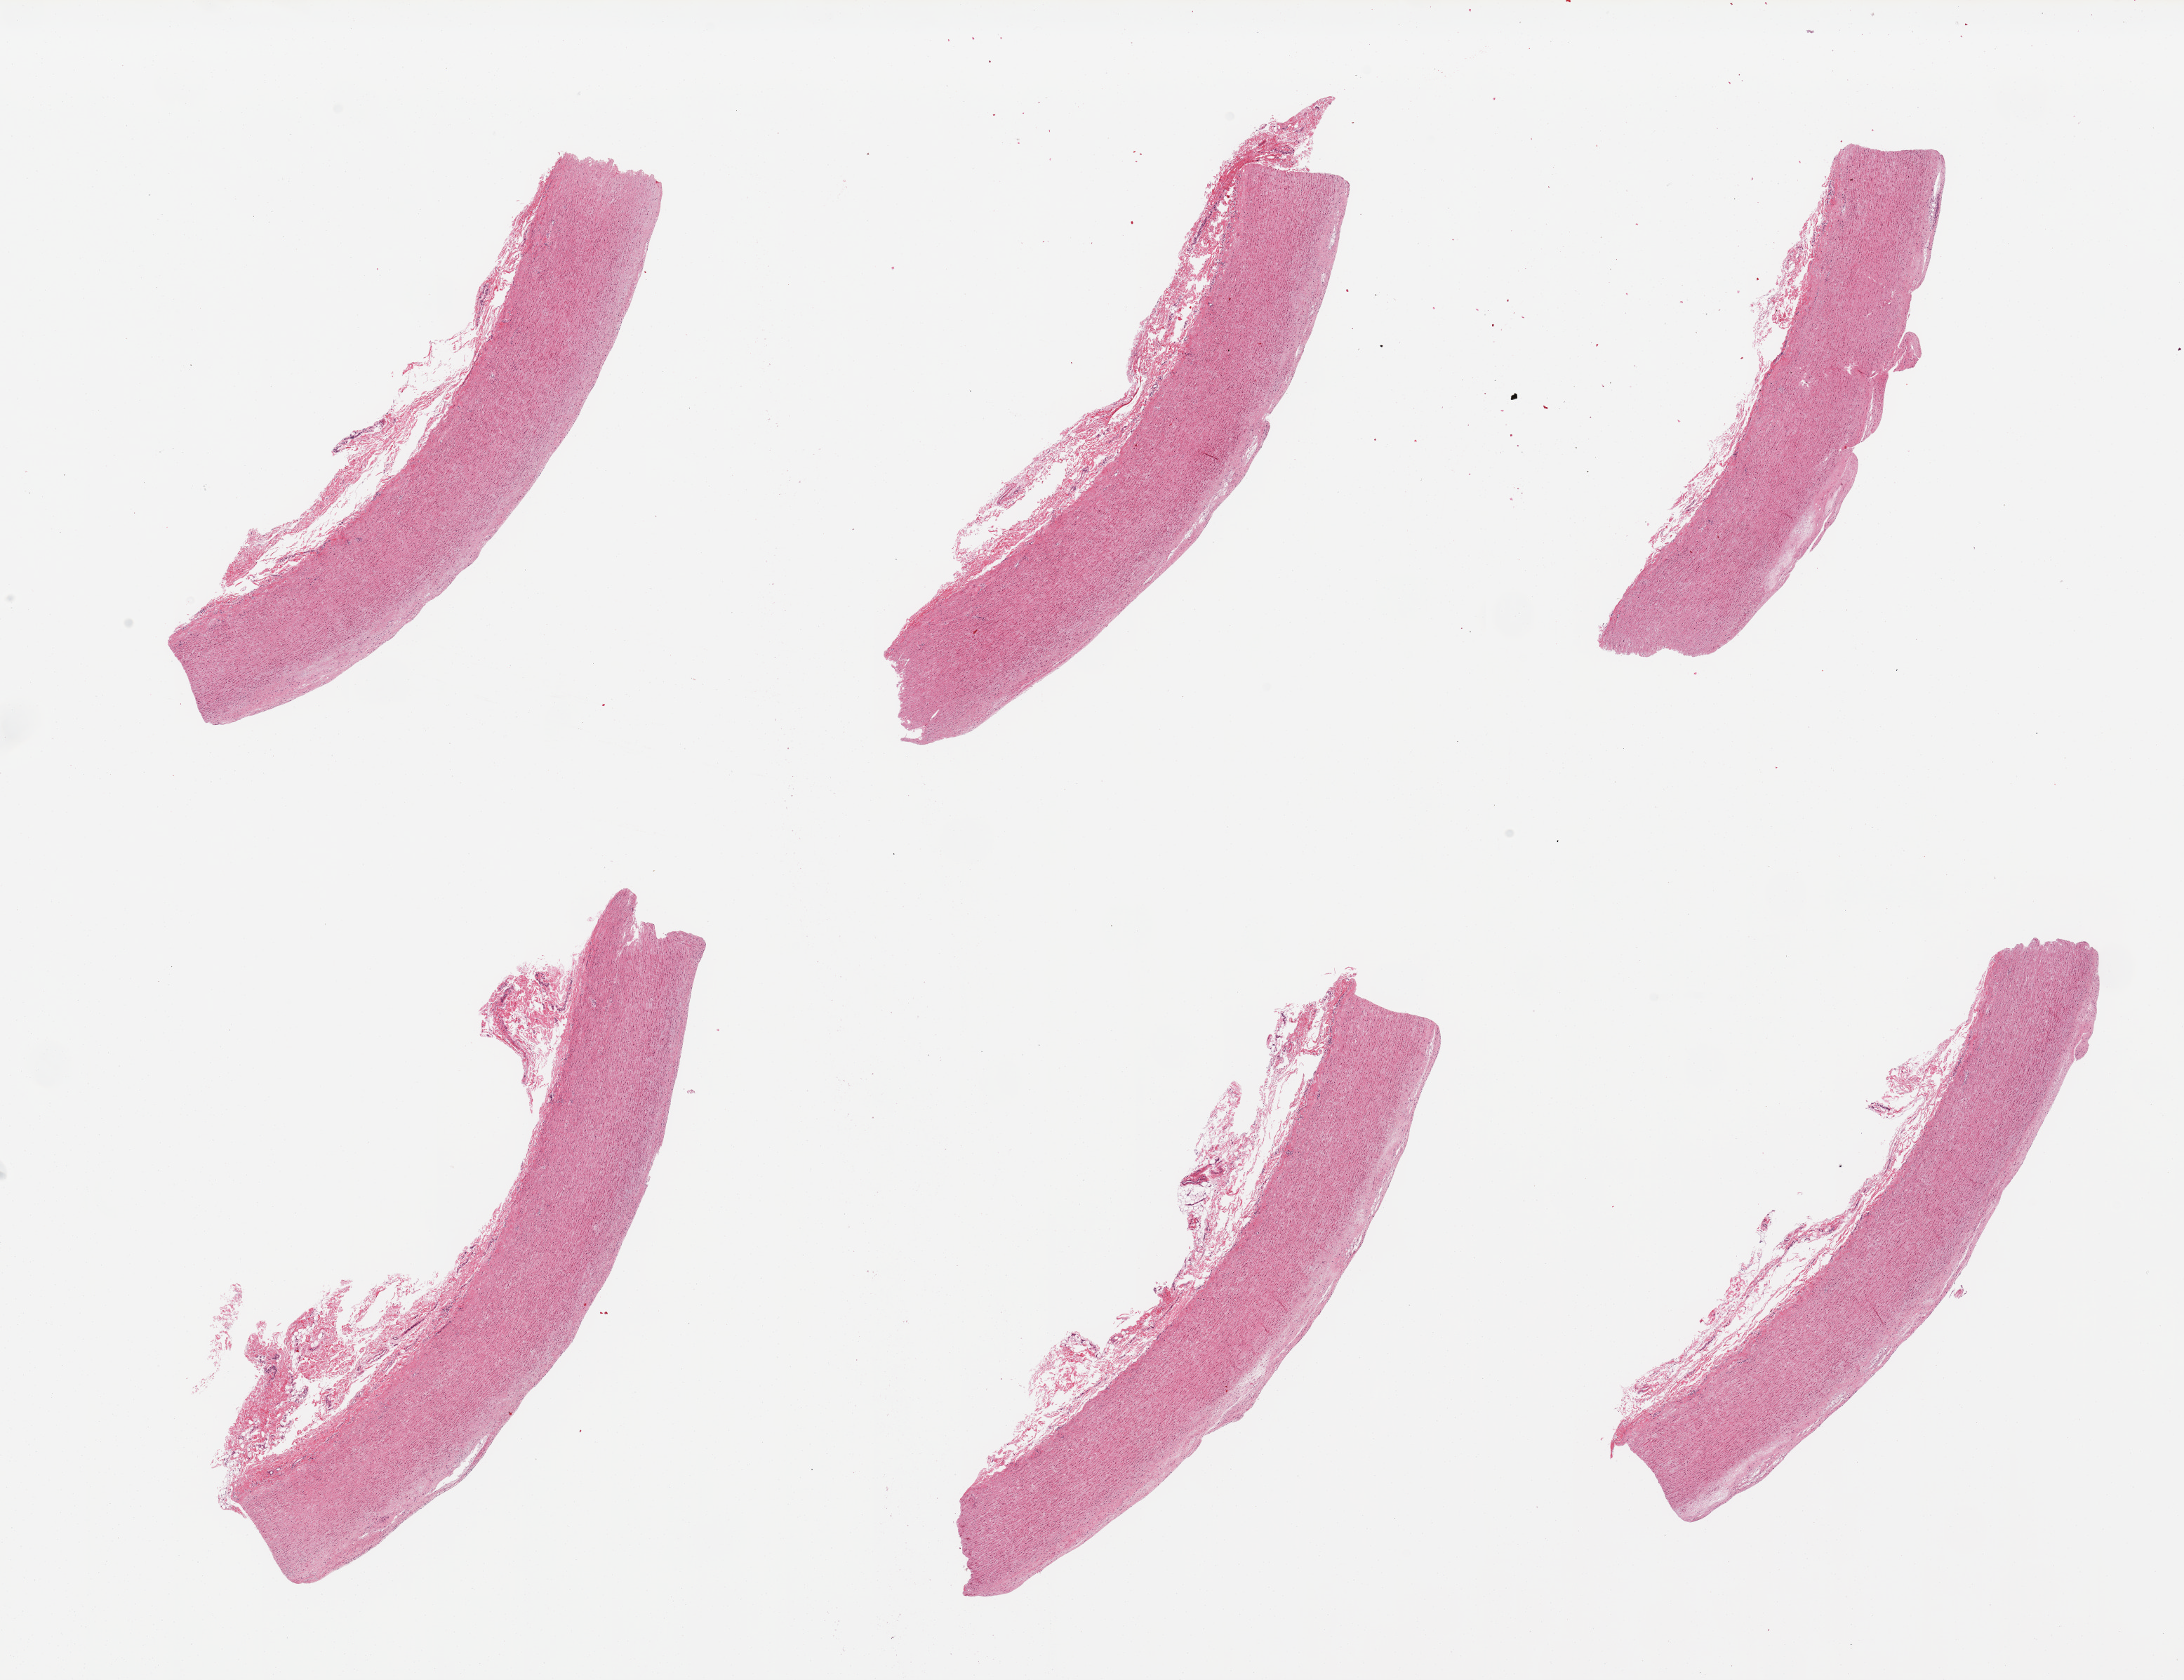
H&E whole-slide image, a low-resolution overview of the entire scanned area, about 24.6 x 18.9 mm; PAXgene-fixed, paraffin-embedded tissue; sampled site (target tissue): coronary artery; donor tissue sample. Female donor.
Review note (as recorded): 6 pieces; aorta NOT coronary artery.